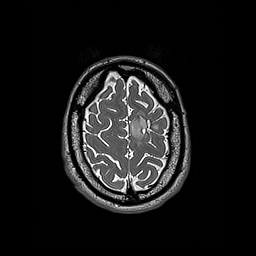
Brain MRI from a brain-tumour surgery series, one axial slice; slice 45 of 192 in the series (ordered by position); 1 mm slice thickness; 256 × 256 image matrix, field of view 250 × 250 mm. From the clinical record (not read from this slice): histopathology: Oligodendroglioma; WHO grade: 3; IDH mutation: yes; tumour location: Left Frontal.
Annotated regions visible in this slice (expert manual segmentation):
- tumour: bounding box (x1, y1, x2, y2) in pixels: (131, 116, 158, 144)